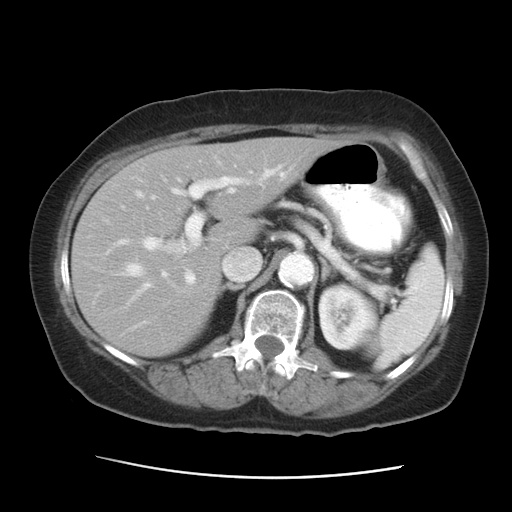
Contrast-enhanced abdominal CT, one axial slice; slice 18 of 29 in the series (ordered by position); intravenous contrast given; soft-tissue window (W 400 / L 40 HU); 7.5 mm slice thickness; 512 × 512 image matrix, field of view 354 × 354 mm. Female patient, age 64 years. From the clinical record (not read from this slice): diagnosis: colorectal cancer liver metastases, imaged before liver resection; multiple liver metastases: no; largest metastasis: 2.5 cm; chemotherapy before resection: no.
Structures marked on this image (expert manual segmentation):
- hepatic veins: box from (x=120, y=164) to (x=293, y=302) px
- liver: (x=72, y=137)–(x=341, y=356)
- planned liver remnant (the part of the liver to remain after resection): (x=72, y=137)–(x=342, y=304)
- portal vein (with intrahepatic branches): (x=115, y=171)–(x=274, y=285)